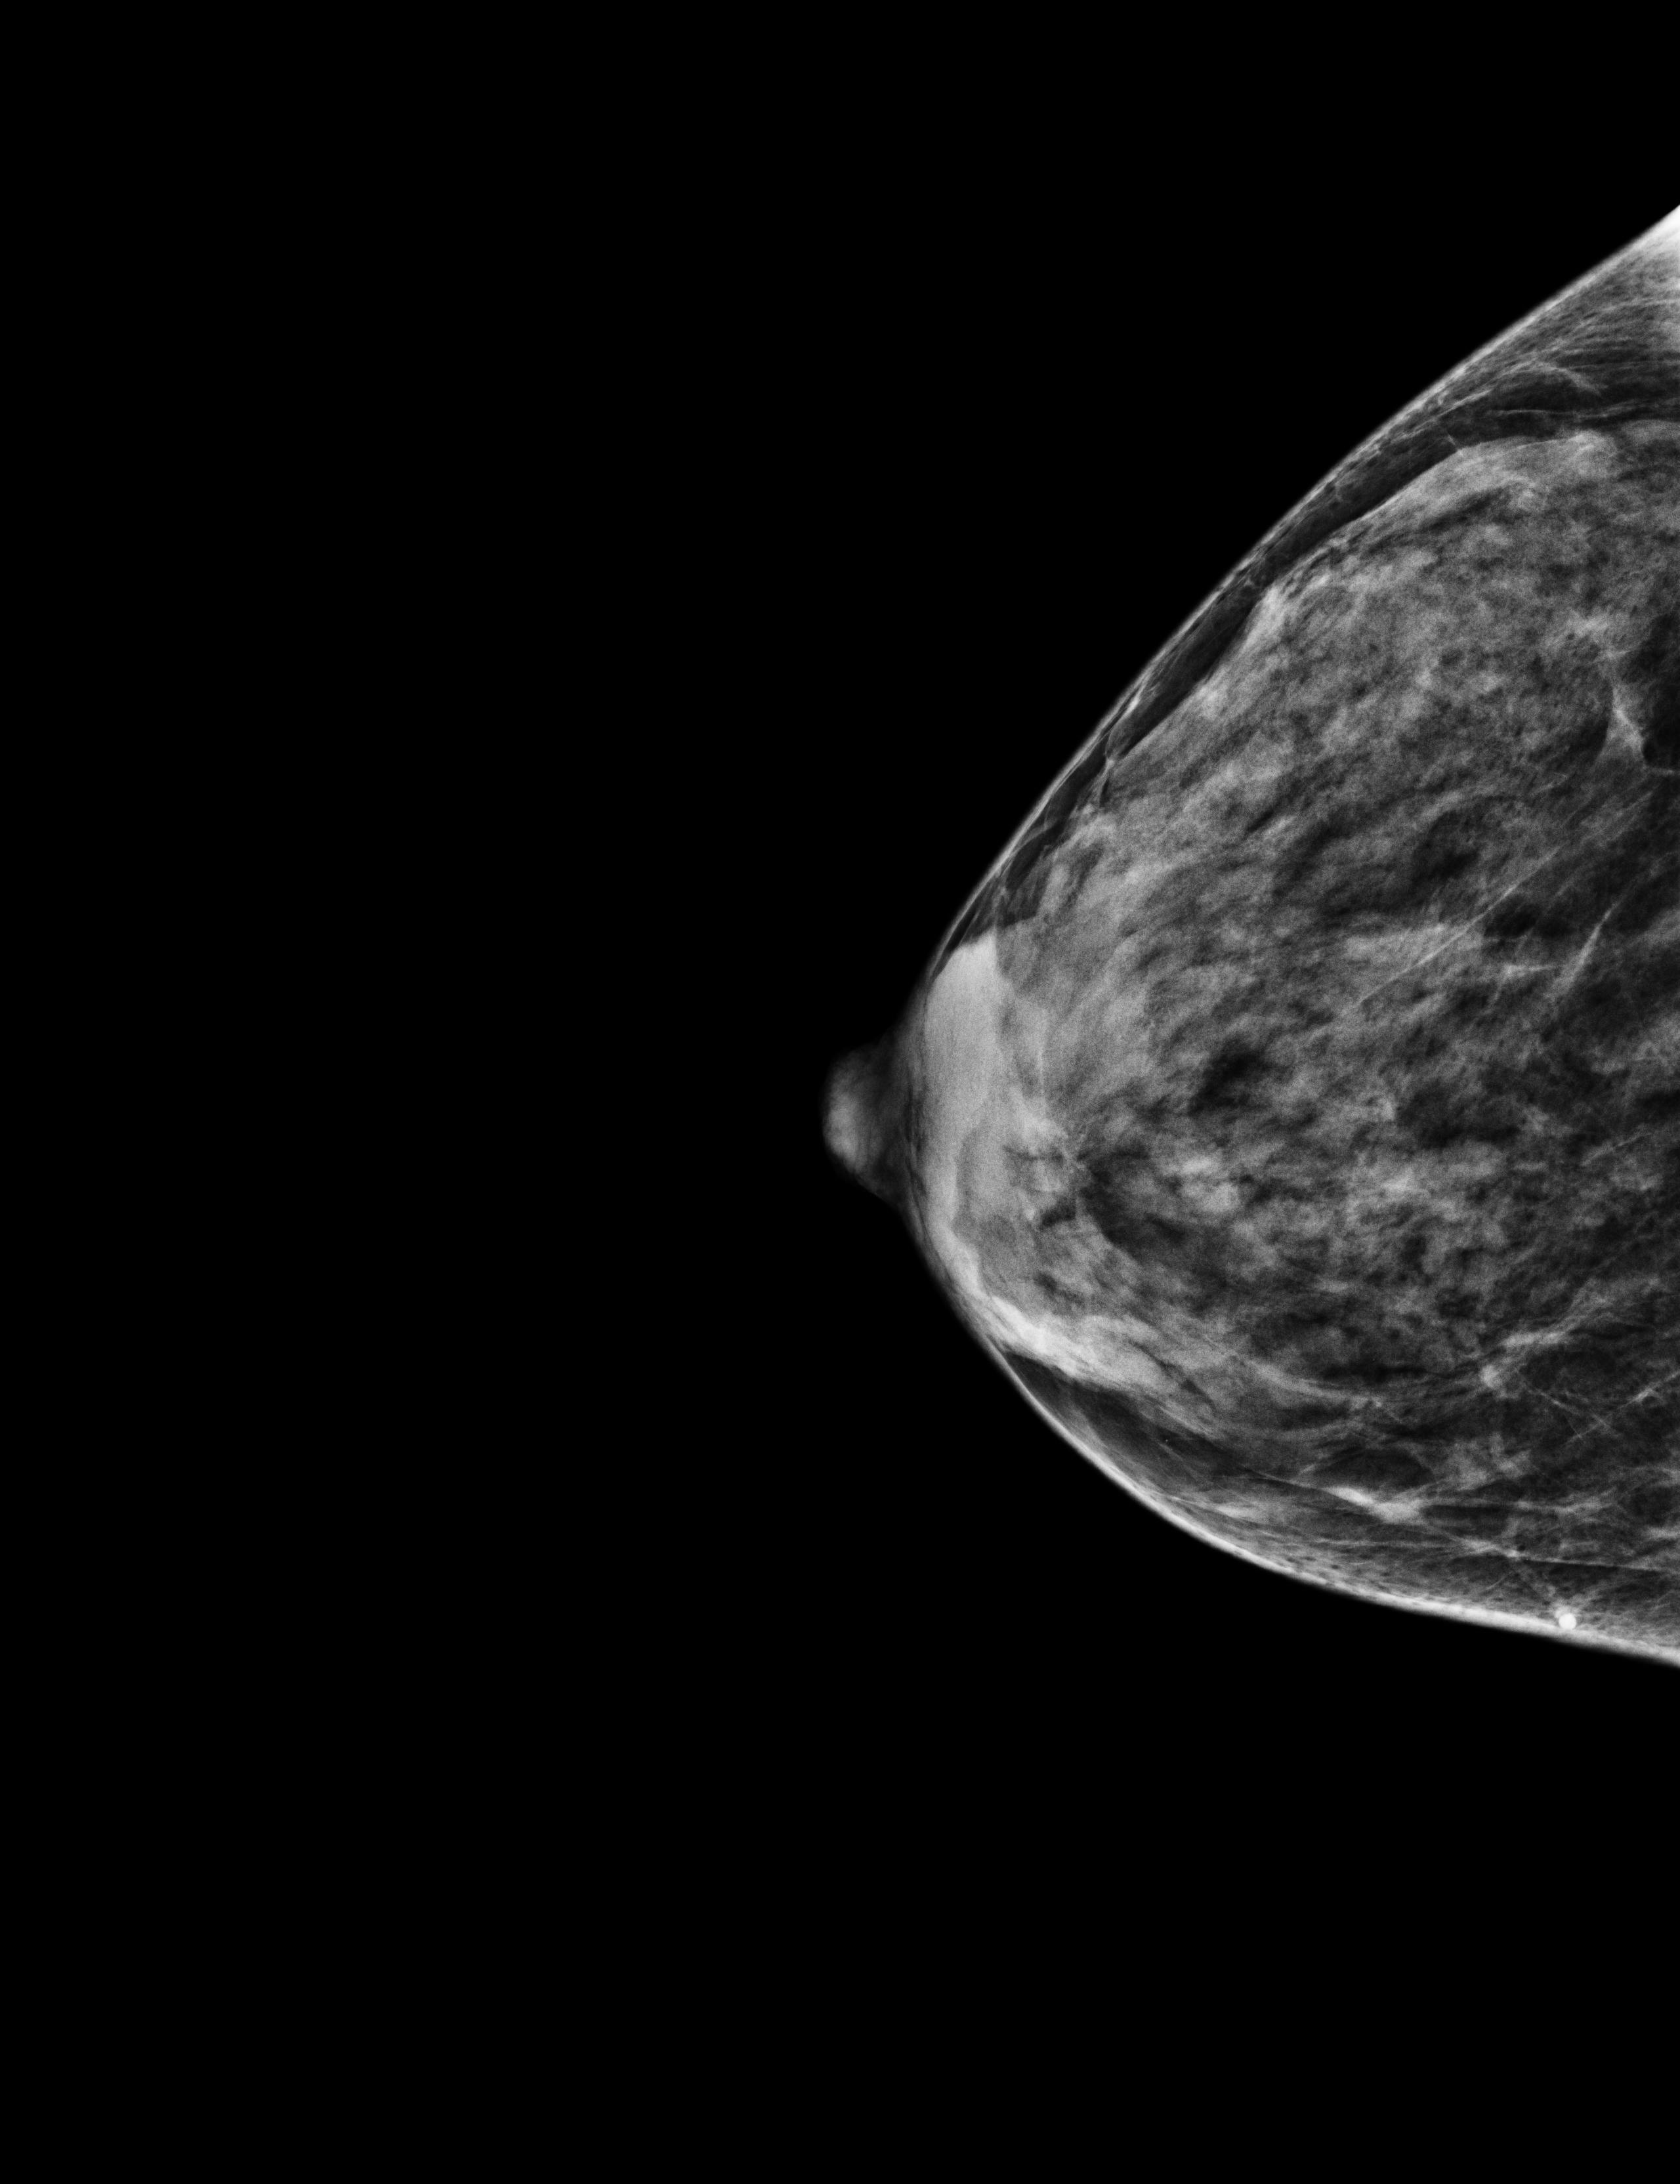
Annual screening mammography examination, compressed breast thickness 33 mm. Patient aged 56 years (female).
Image type: full-field digital mammogram. Breast: right. Projection: cranio-caudal projection.